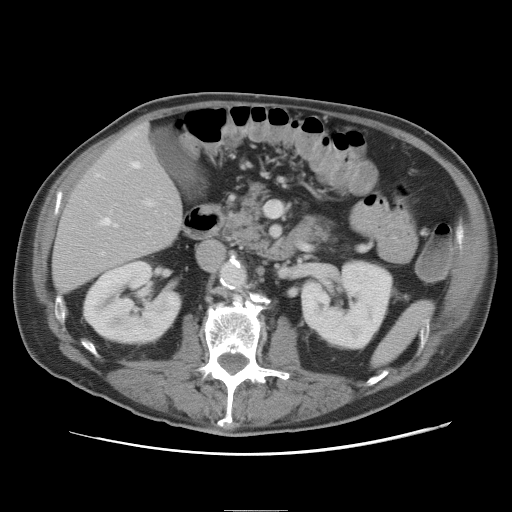
Contrast-enhanced abdominal CT, one axial slice. Position 28 of 89 along the scan axis. Intravenous contrast given. Soft-tissue window (W 400 / L 40 HU). 5 mm slice thickness. 512 × 512 image matrix. Male patient, age 69 years. Case-level facts recorded for this patient, not image findings: diagnosis: colorectal cancer liver metastases, imaged before liver resection; multiple liver metastases: no; largest metastasis: 8.5 cm; disease in both lobes: no.
Outlined on this slice (outlined manually by an expert reader):
- hepatic veins: box from (x=97, y=161) to (x=141, y=226) px
- liver: (x=54, y=123)–(x=183, y=292)
- planned liver remnant (the part of the liver to remain after resection): (x=54, y=123)–(x=183, y=292)
- portal vein (with intrahepatic branches): (x=102, y=199)–(x=155, y=254)